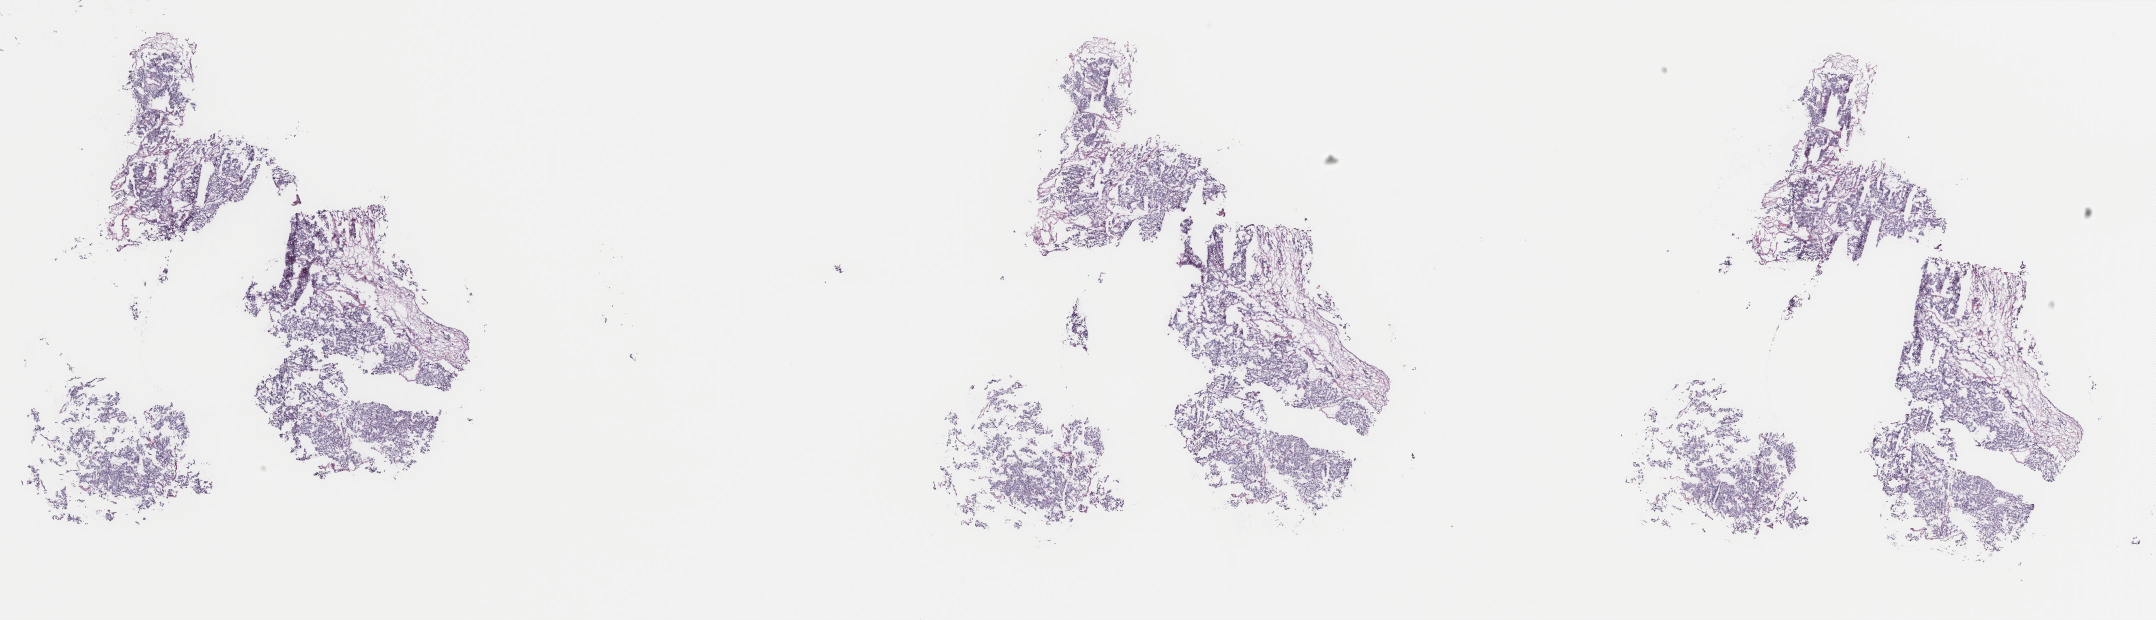
Whole-slide histology image, Hematoxylin and eosin (H&E) stained — a low-resolution overview of the entire scanned area, about 34.2 x 9.8 mm (slide scanned at 40x). Frozen section. Primary tumour sample from the adrenal gland. Female, age 53 years at initial diagnosis. Composition of this section per pathologist review: tumour cells 90%, tumour nuclei 95%, normal cells 0%, stromal cells 10%, necrosis 0%. Inflammatory infiltration, as recorded: lymphocyte infiltration 0%, monocyte infiltration 0%, neutrophil infiltration 0%.
- histologic diagnosis: Pheochromocytoma, NOS
- laterality: right